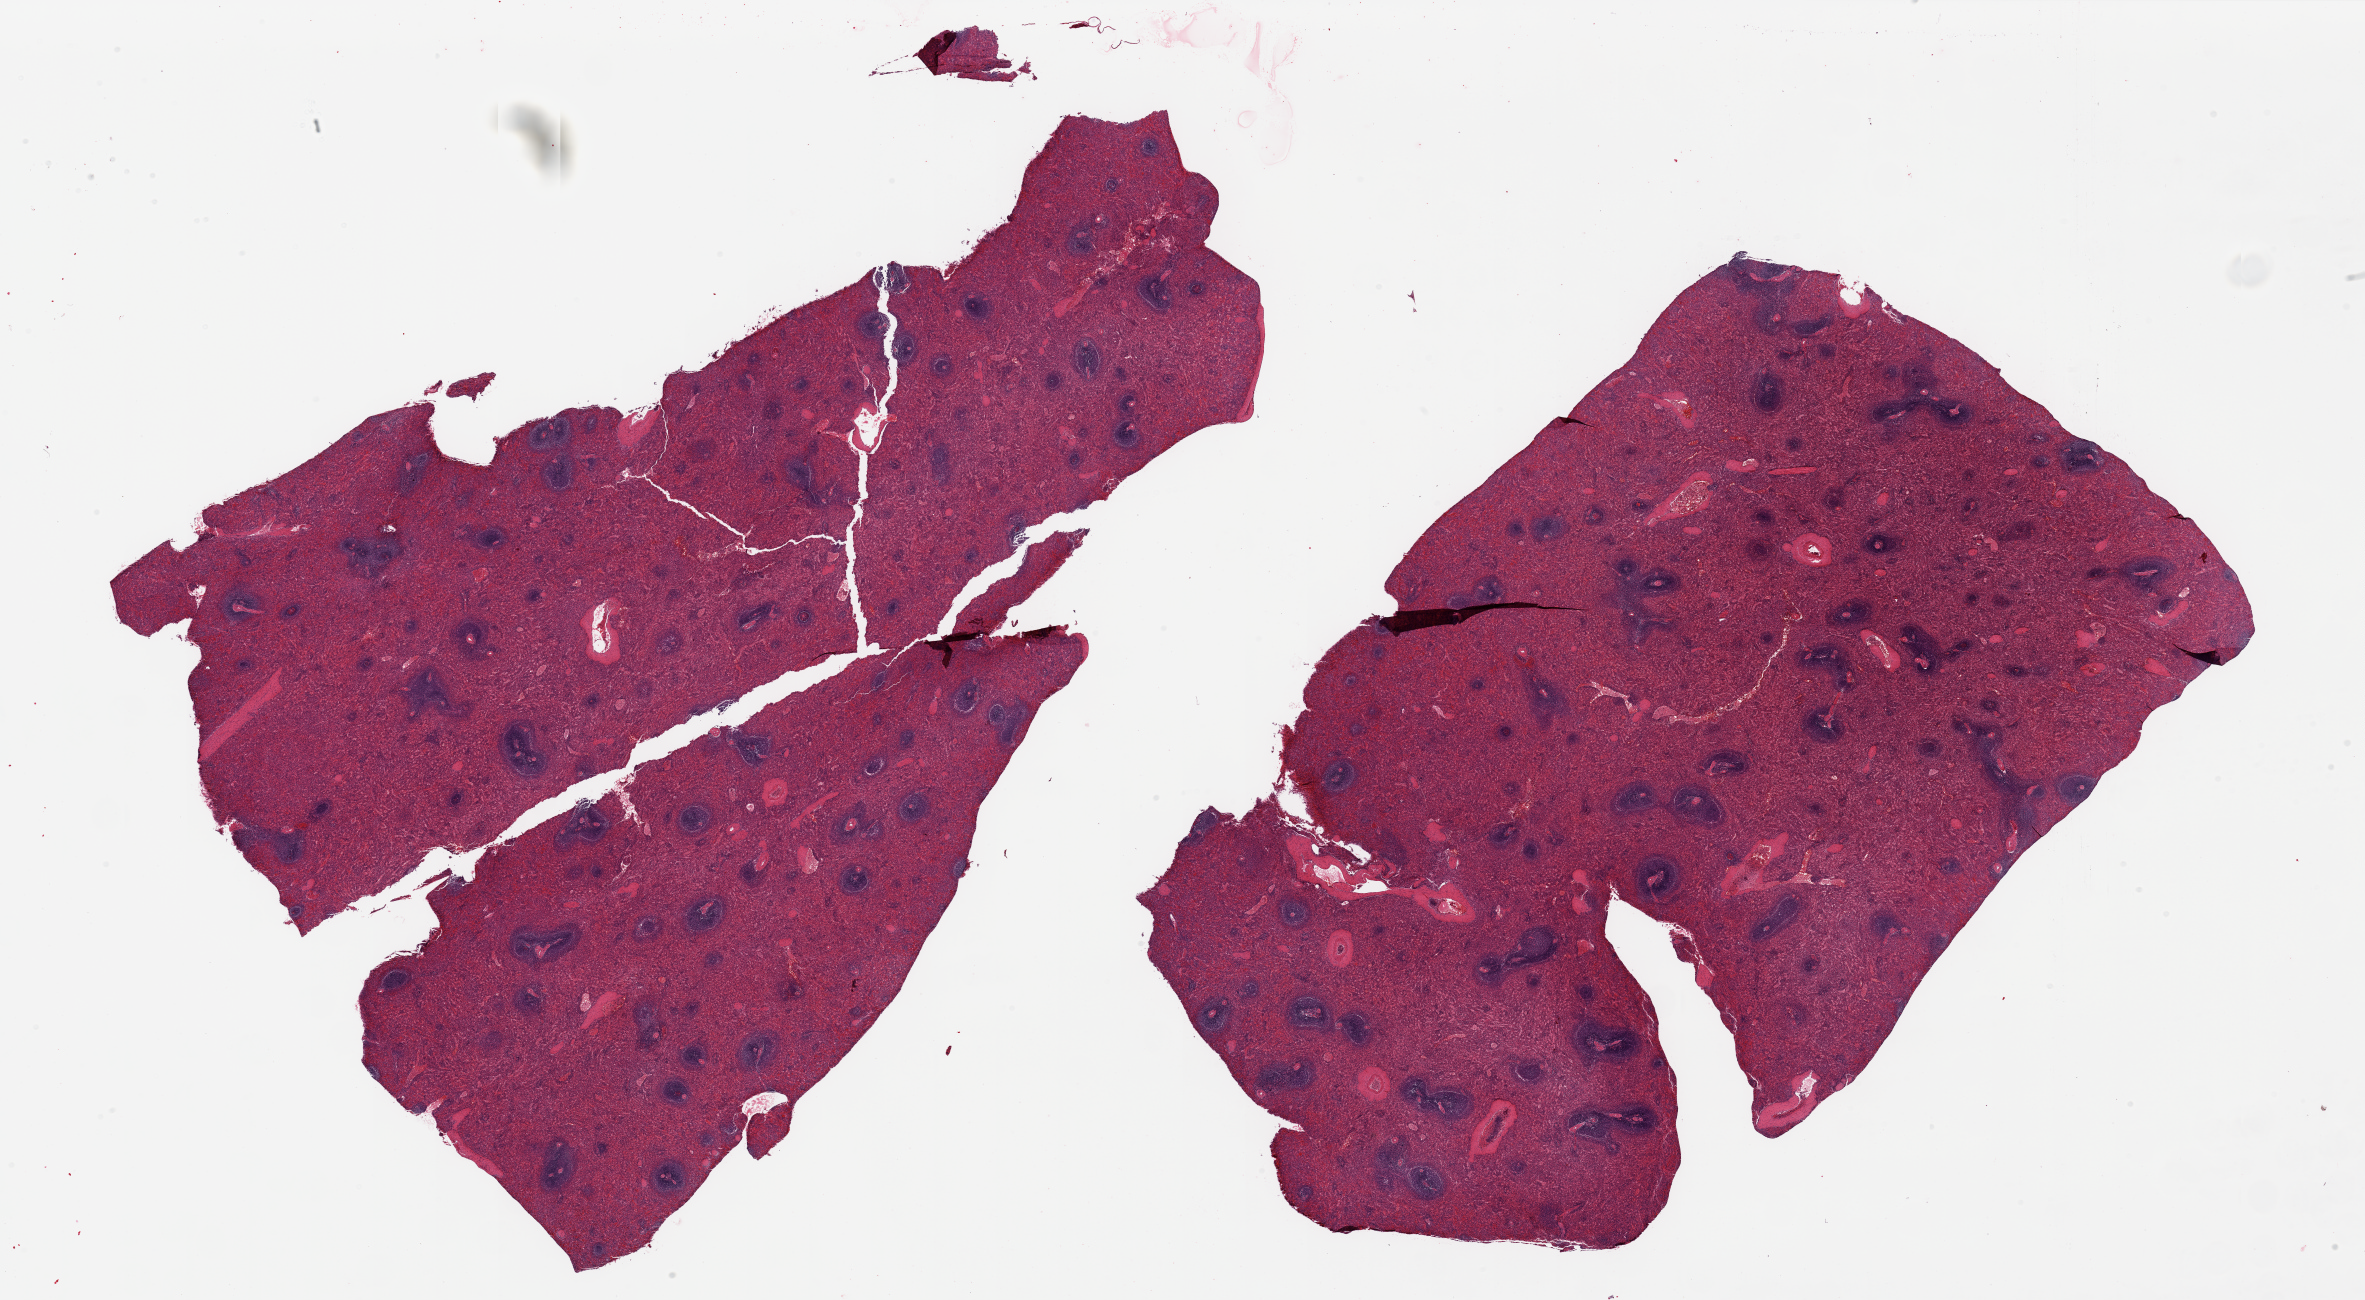
Whole-slide image, haematoxylin and eosin stain — whole scanned area (about 37.4 x 20.6 mm) shown as a low-resolution overview, PAXgene-fixed paraffin-embedded (PFPE) section, section of spleen (target tissue), donor tissue sample. Donor sex: male.
Pathologist's review note for this sample: 2 pieces, no abnormalities.